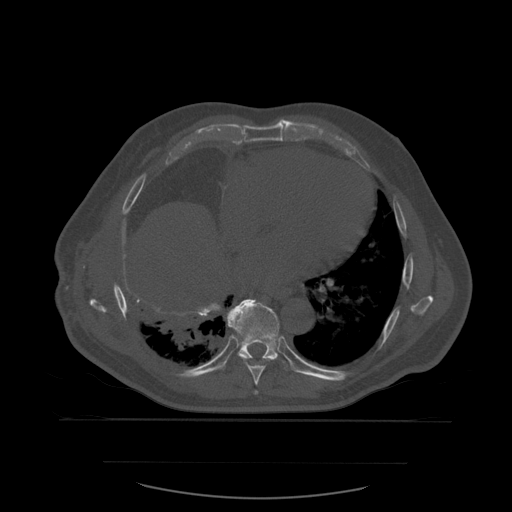
CT including the spine, one axial slice; bone window (W 1800 / L 400 HU); 1.25 mm slice thickness; 512 × 512 image matrix, field of view 479 × 479 mm. Patient age 71 years. Case-level facts recorded for this patient, not image findings: primary cancer: lung; vertebrae with lytic lesions (as recorded): T1, T2, L5, S1.
Annotated regions visible in this slice (semi-automatic segmentation, software-assisted and operator-edited):
- T8 vertebra: bounding box (x1, y1, x2, y2) in pixels: (227, 312, 278, 395)
- T9 vertebra: (223, 299, 294, 371)